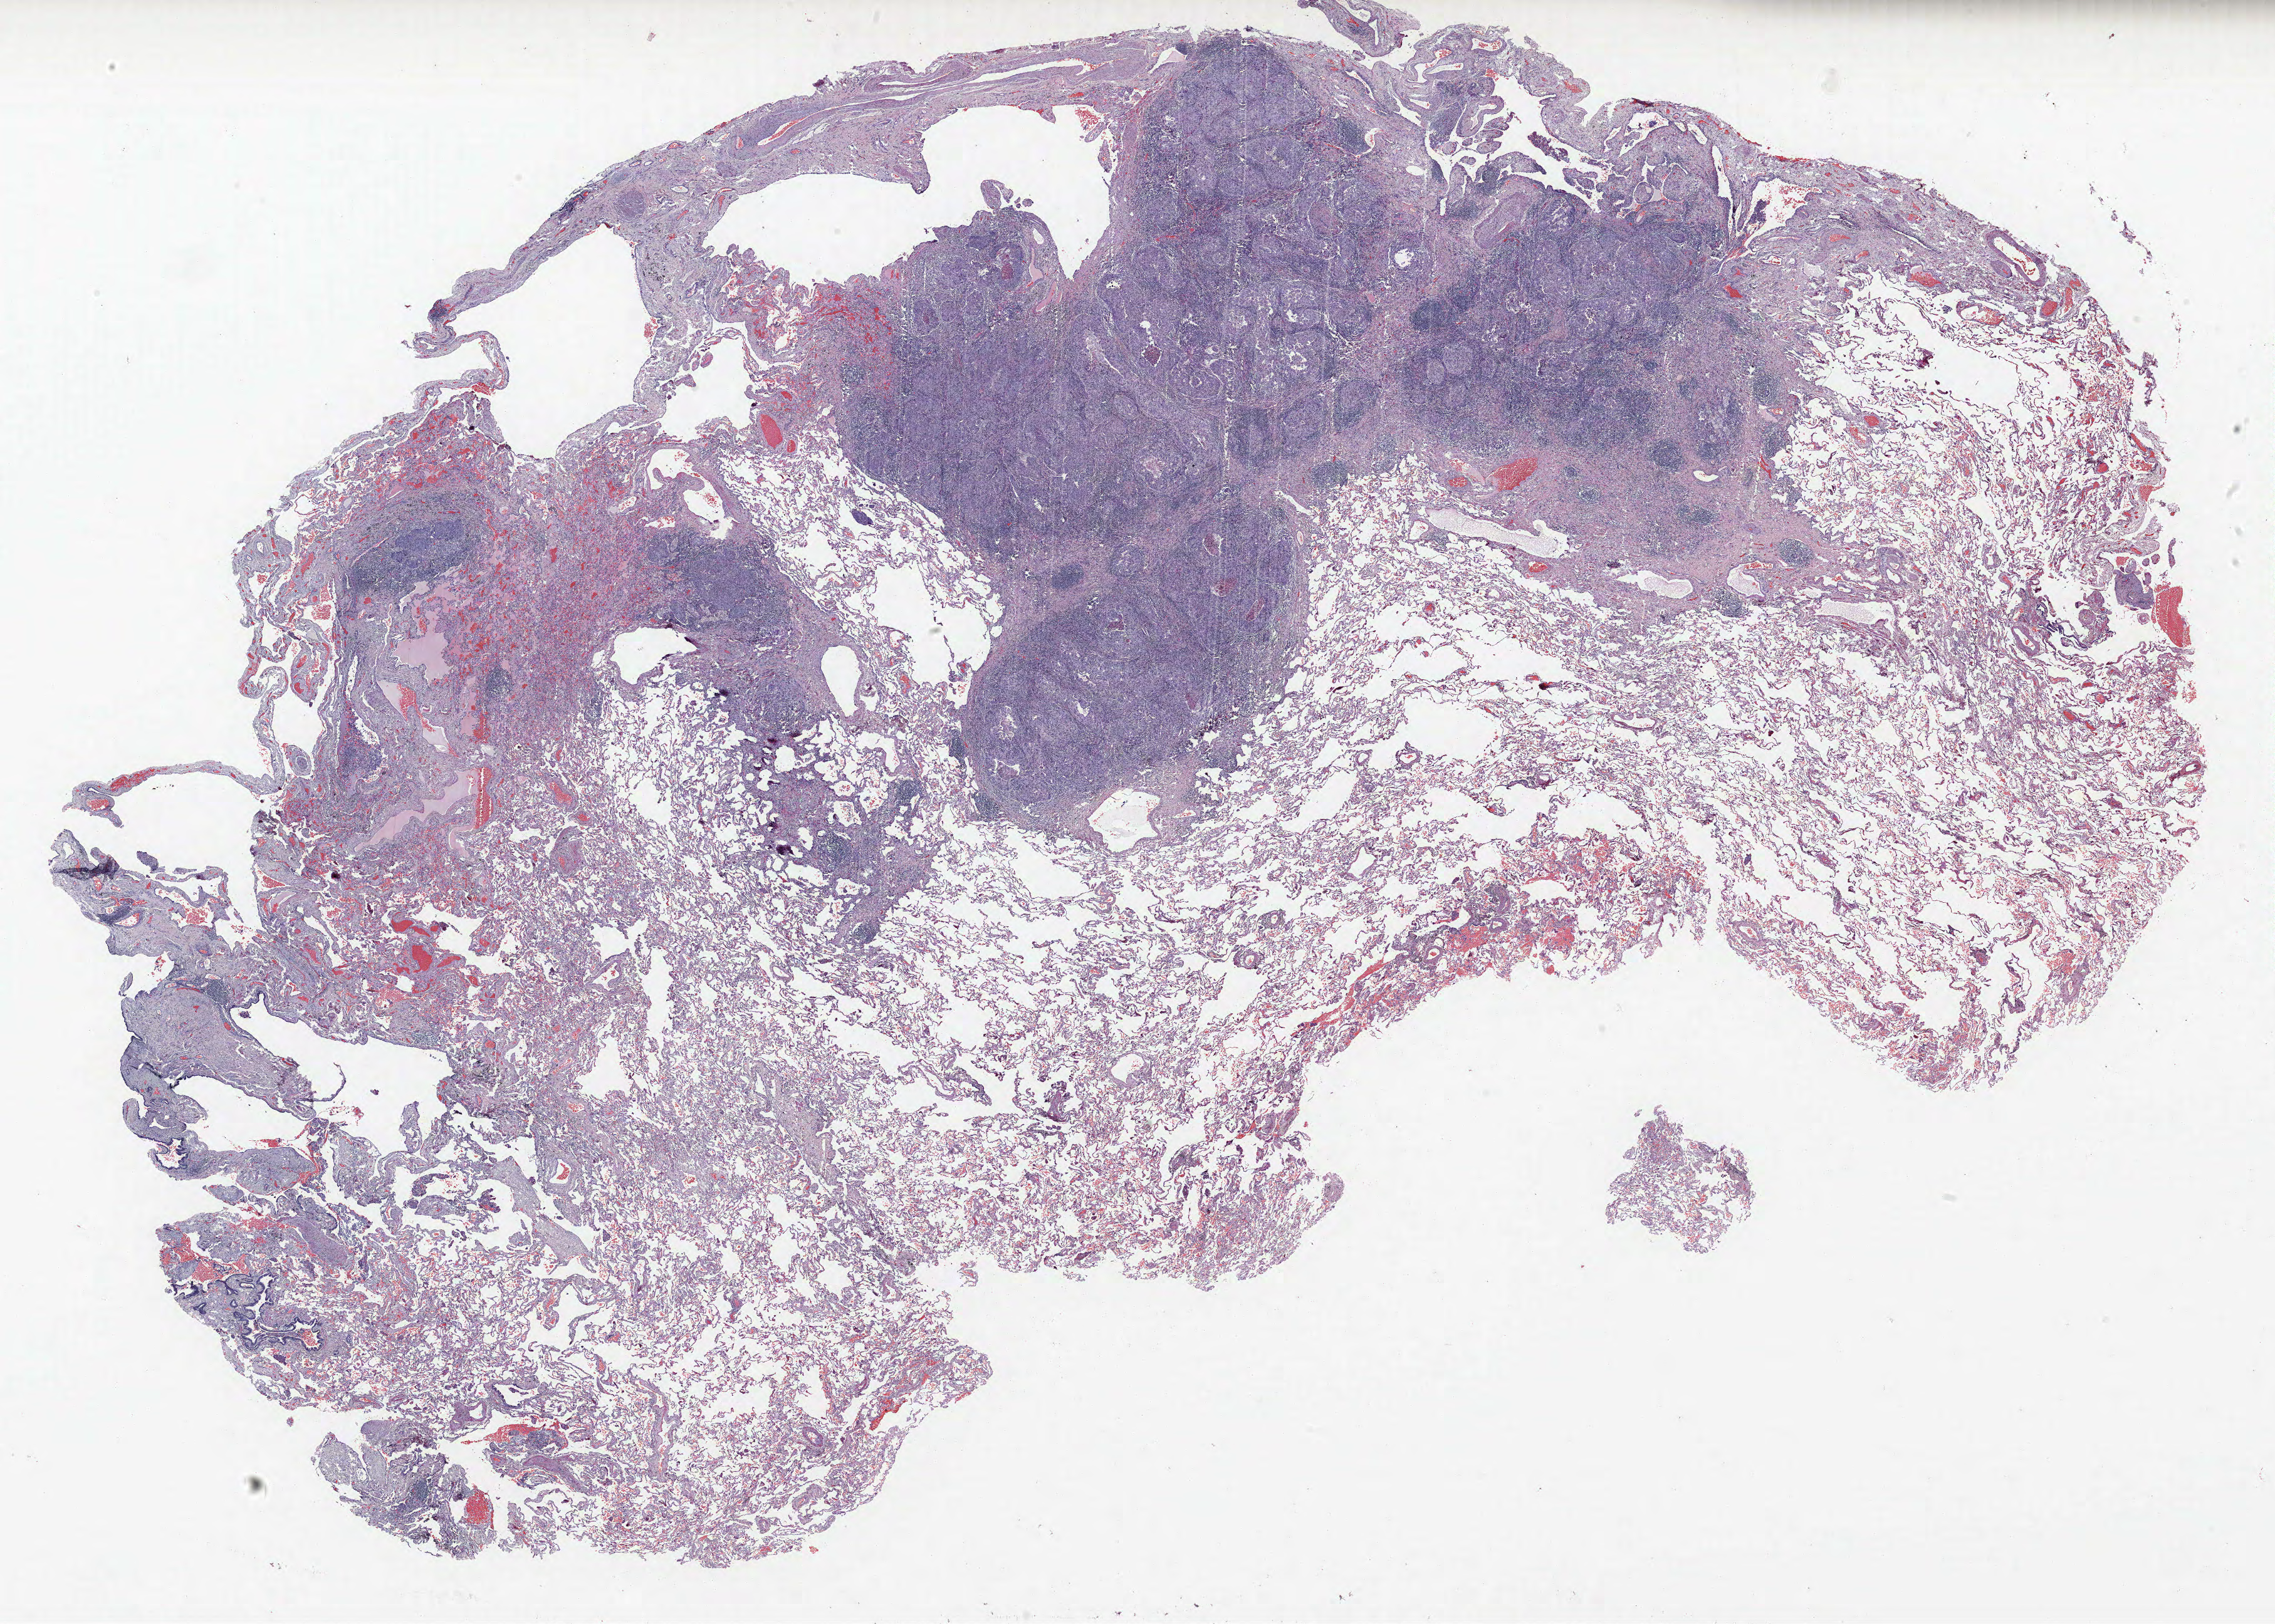
Hematoxylin and eosin (H&E) stained whole-slide image — whole scanned area (about 29.0 x 20.7 mm) shown as a low-resolution overview. Formalin-fixed paraffin-embedded (FFPE) section. Lung tissue. Male, age 61 at enrolment. Former smoker at enrolment. Grade: poorly differentiated (G3).
ICD-O-3 topography: upper lobe of lung (C34.1). Tumour size (pathology): 20 mm. Stage (AJCC 6th edition): IA. Primary tumour location (clinical record): right upper lobe. Participant's lung-cancer diagnosis: Squamous cell carcinoma, NOS.